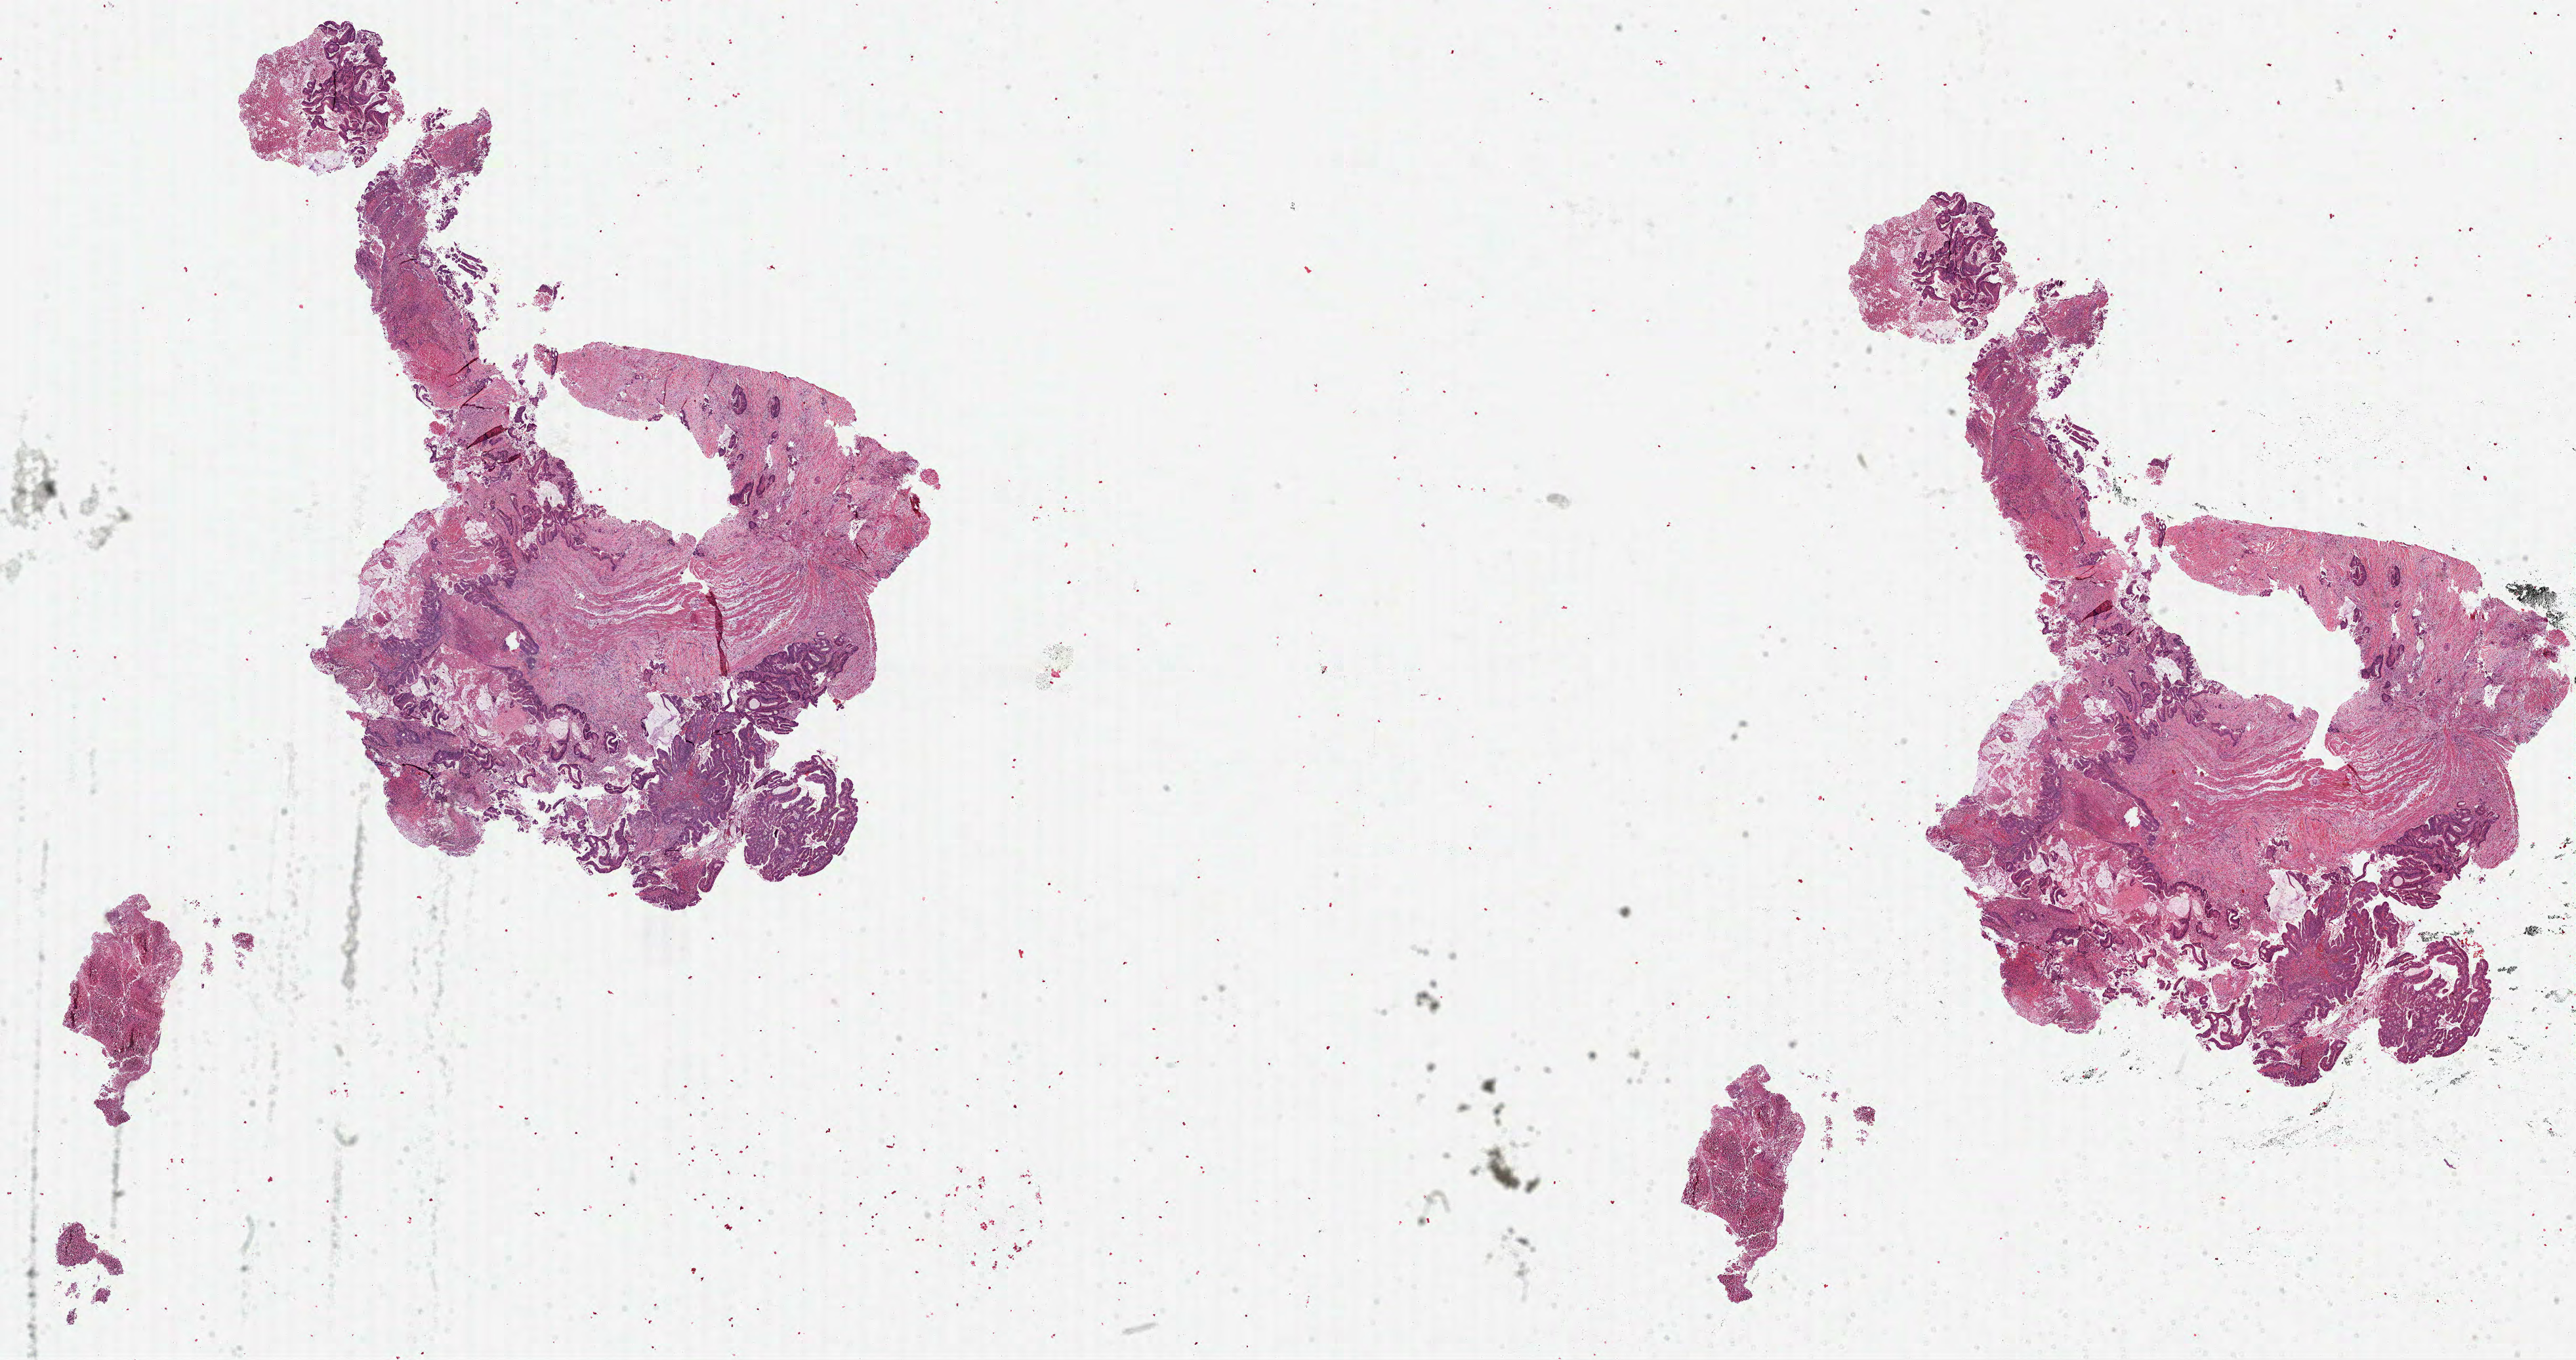
Digitized H&E tissue section (whole slide) — low-resolution overview of the scanned area, about 31.7 x 16.7 mm (from a 40x scan). FFPE section. Primary tumour sample from the colon. Patient: male, age at initial diagnosis 70 years.
Diagnosis: Adenocarcinoma, NOS. AJCC pathologic stage: IV (6th edition). Lymph nodes positive (case pathology): 2 of 13 examined. TNM: T4b N1 M1.